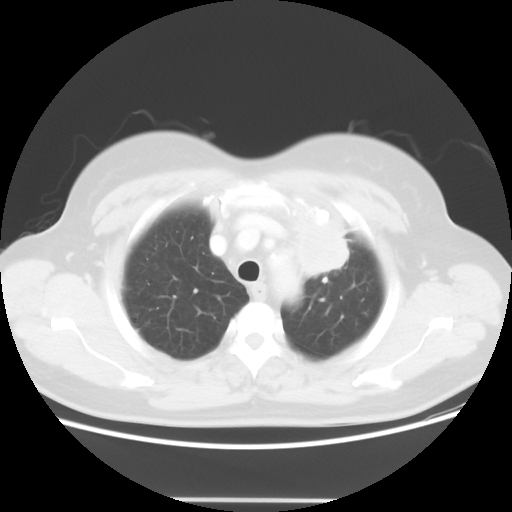
Chest CT, one axial slice. Slice 44 of 52 in the series (ordered by position). Reconstruction kernel STANDARD. 120 kVp. Lung window (W 1500 / L -600 HU). 5 mm slice thickness. 512 × 512 image matrix. Patient: female, 52 years. From the clinical record (not read from this slice): clinical TNM (as recorded): T2 N3 M0.
Annotated regions visible in this slice (bounding box drawn by a radiologist):
- lung tumour (recorded histology: adenocarcinoma): bounding box [x1, y1, x2, y2] px = [289, 211, 355, 278]